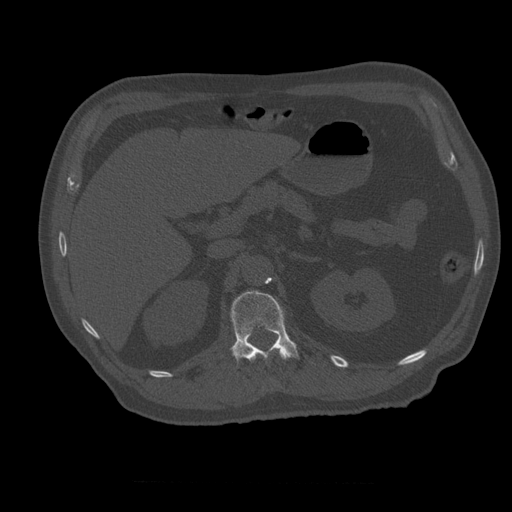
CT including the spine, one axial slice. Slice 241 of 399 in the series (ordered by position). 120 kVp. Bone window (W 1800 / L 400 HU). 1.25 mm slice thickness. 512 × 512 image matrix. Patient age 73 years. Case-level facts recorded for this patient, not image findings: primary cancer: prostate; vertebrae with lytic lesions (as recorded): L2.
Structures marked on this image (semi-automatically segmented with operator editing):
- L1 vertebra: bounding box [x1, y1, x2, y2] px = [231, 291, 299, 361]
- T12 vertebra: [250, 349, 291, 362]